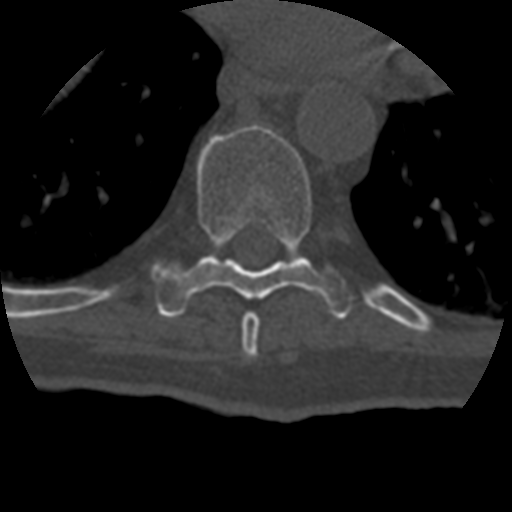
CT including the spine, one axial slice; slice 240 of 399 in the series (ordered by position); reconstruction kernel STANDARD; 120 kVp; bone window (W 1800 / L 400 HU); 512 × 512 image matrix, field of view 160 × 160 mm. Patient age 69 years. Case-level facts recorded for this patient, not image findings: primary cancer: prostate.
Annotated regions visible in this slice (semi-automatic segmentation, software-assisted and operator-edited):
- T8 vertebra: bounding box [x1, y1, x2, y2] px = [242, 312, 260, 358]
- T9 vertebra: [153, 125, 354, 319]